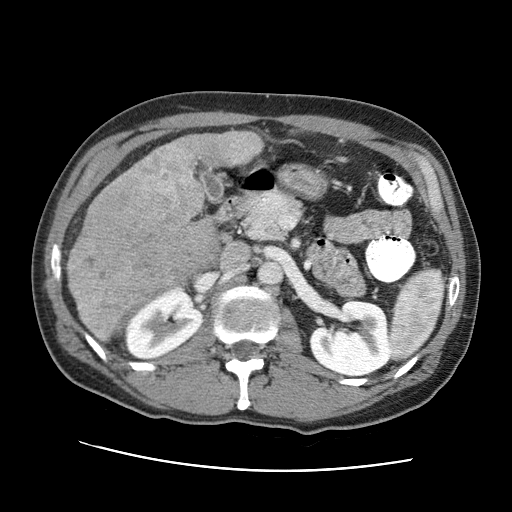
Contrast-enhanced abdominal CT (liver protocol), one axial slice. Position 33 of 95 along the scan axis. One of 2 acquisitions stored at this slice position. Soft-tissue window (W 400 / L 40 HU). 2.5 mm slice thickness. 512 × 512 image matrix, field of view 360 × 360 mm. Case-level facts recorded for this patient, not image findings: diagnosis: hepatocellular carcinoma (patient treated with transarterial chemoembolisation; whether this scan precedes or follows treatment is not stated here); TNM stage (as recorded): Stage-IVA; Child-Pugh class: A.
Outlined on this slice (semi-automatically segmented with operator editing):
- liver parenchyma outside the tumour (the mass and vessels are separate outlines, so this box may not span the whole liver): bounding box [x1, y1, x2, y2] px = [94, 132, 262, 340]
- mass: [66, 144, 221, 342]
- liver vessels: [231, 140, 253, 163]